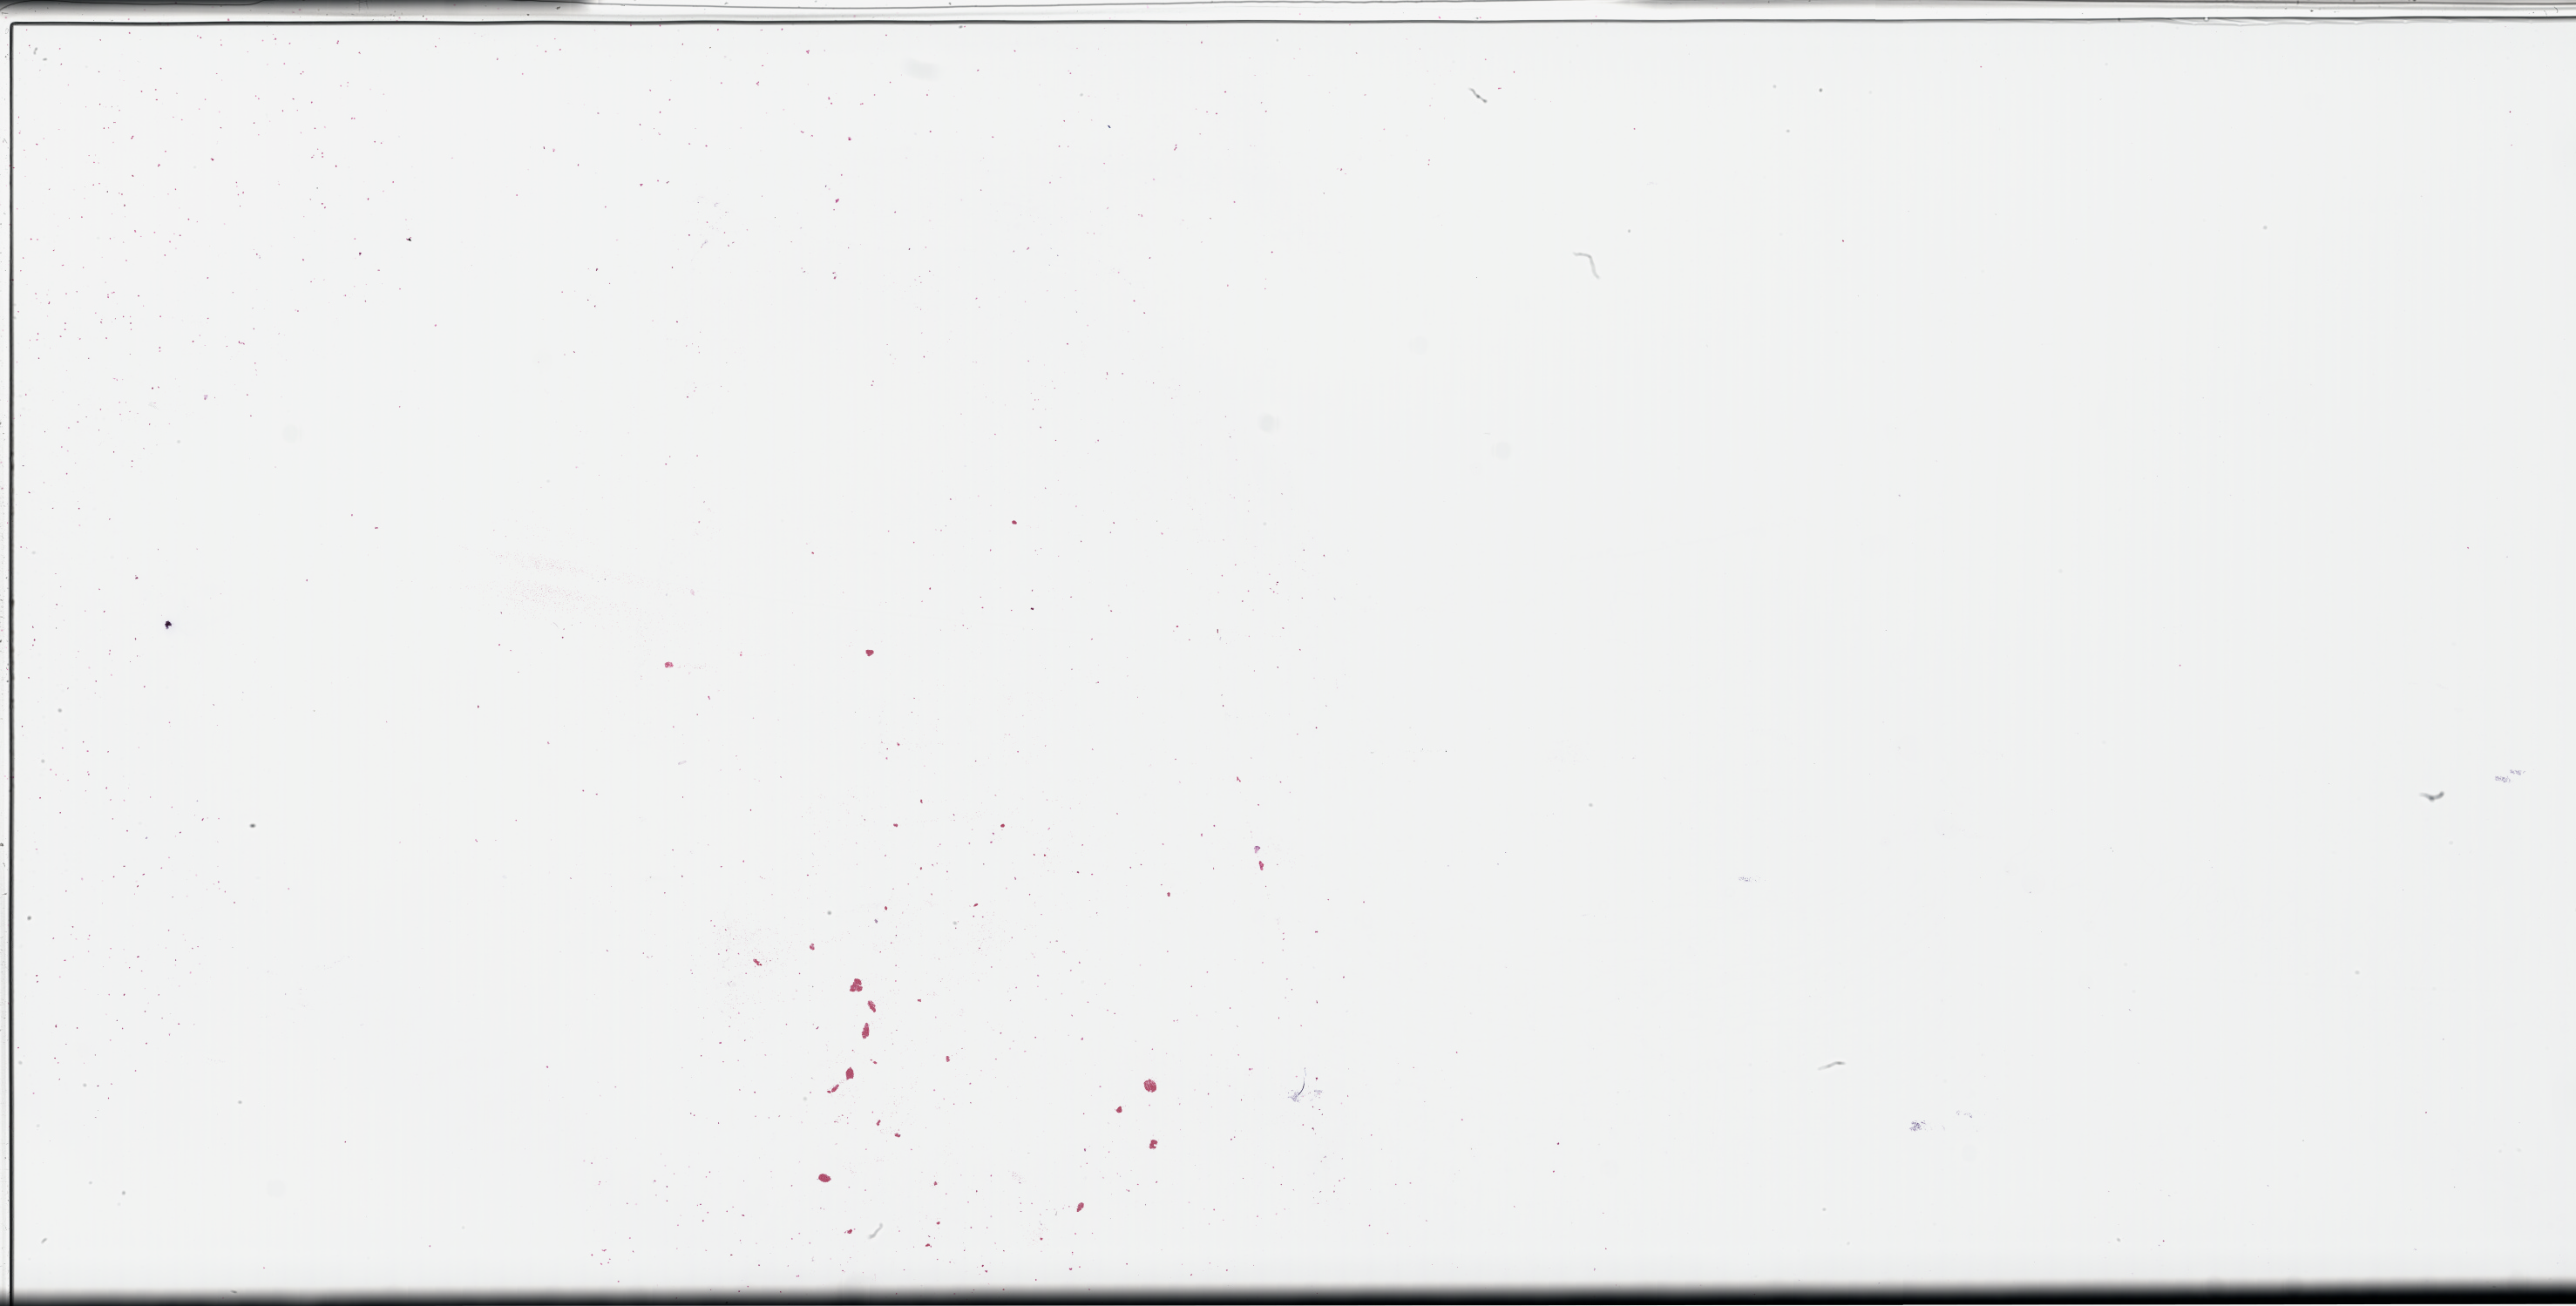
Whole-slide image, hematoxylin and eosin (H&E) stain — whole scanned area (about 47.7 x 24.2 mm) shown as a low-resolution overview; formalin-fixed paraffin-embedded section; archival tissue. Patient sex: male.
This section: metastasis (sampled organ not recorded). Primary diagnosis of the patient: Non-Small Cell Lung Carcinoma.